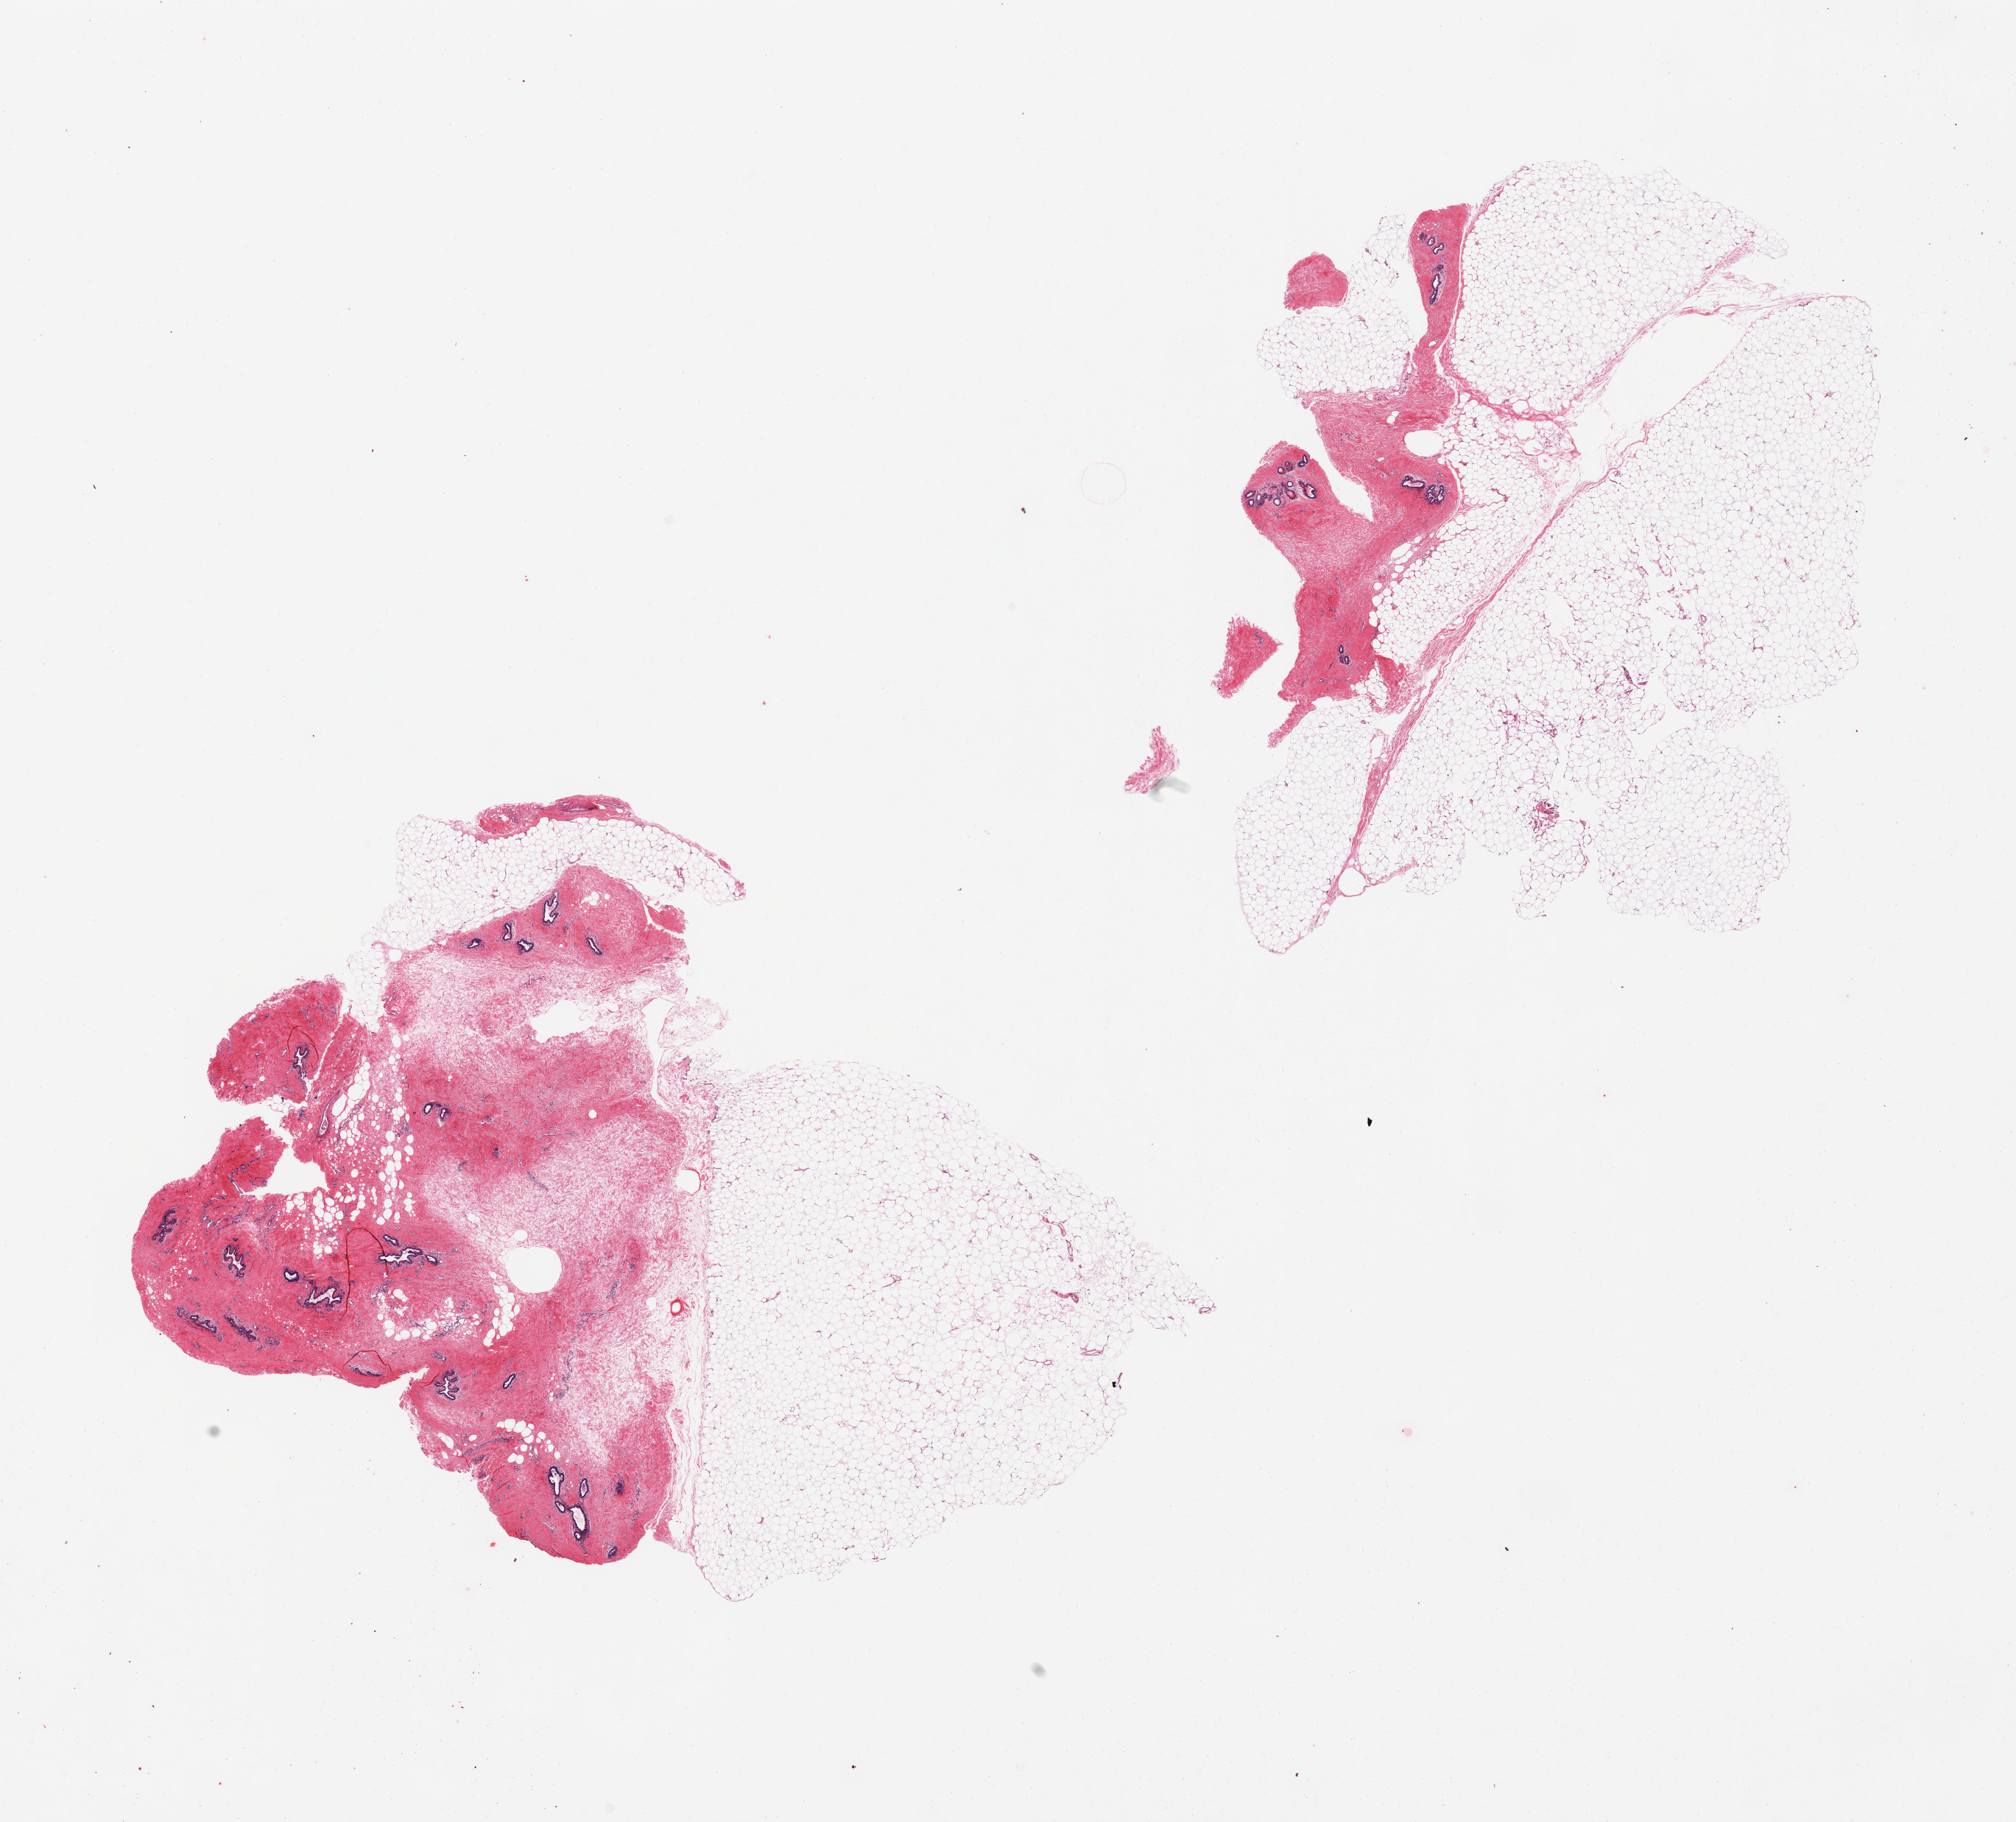
H&E whole-slide image, a low-resolution overview of the entire scanned area, about 21.7 x 19.6 mm (acquisition: 20x scan), PAXgene-fixed, paraffin-embedded tissue, sampled site (target tissue): breast, donor tissue sample. Female donor.
- review note (as recorded): 2 pieces; 1 piece with ducts and atrophic lobules; 1 with 80%, other with 50% fat